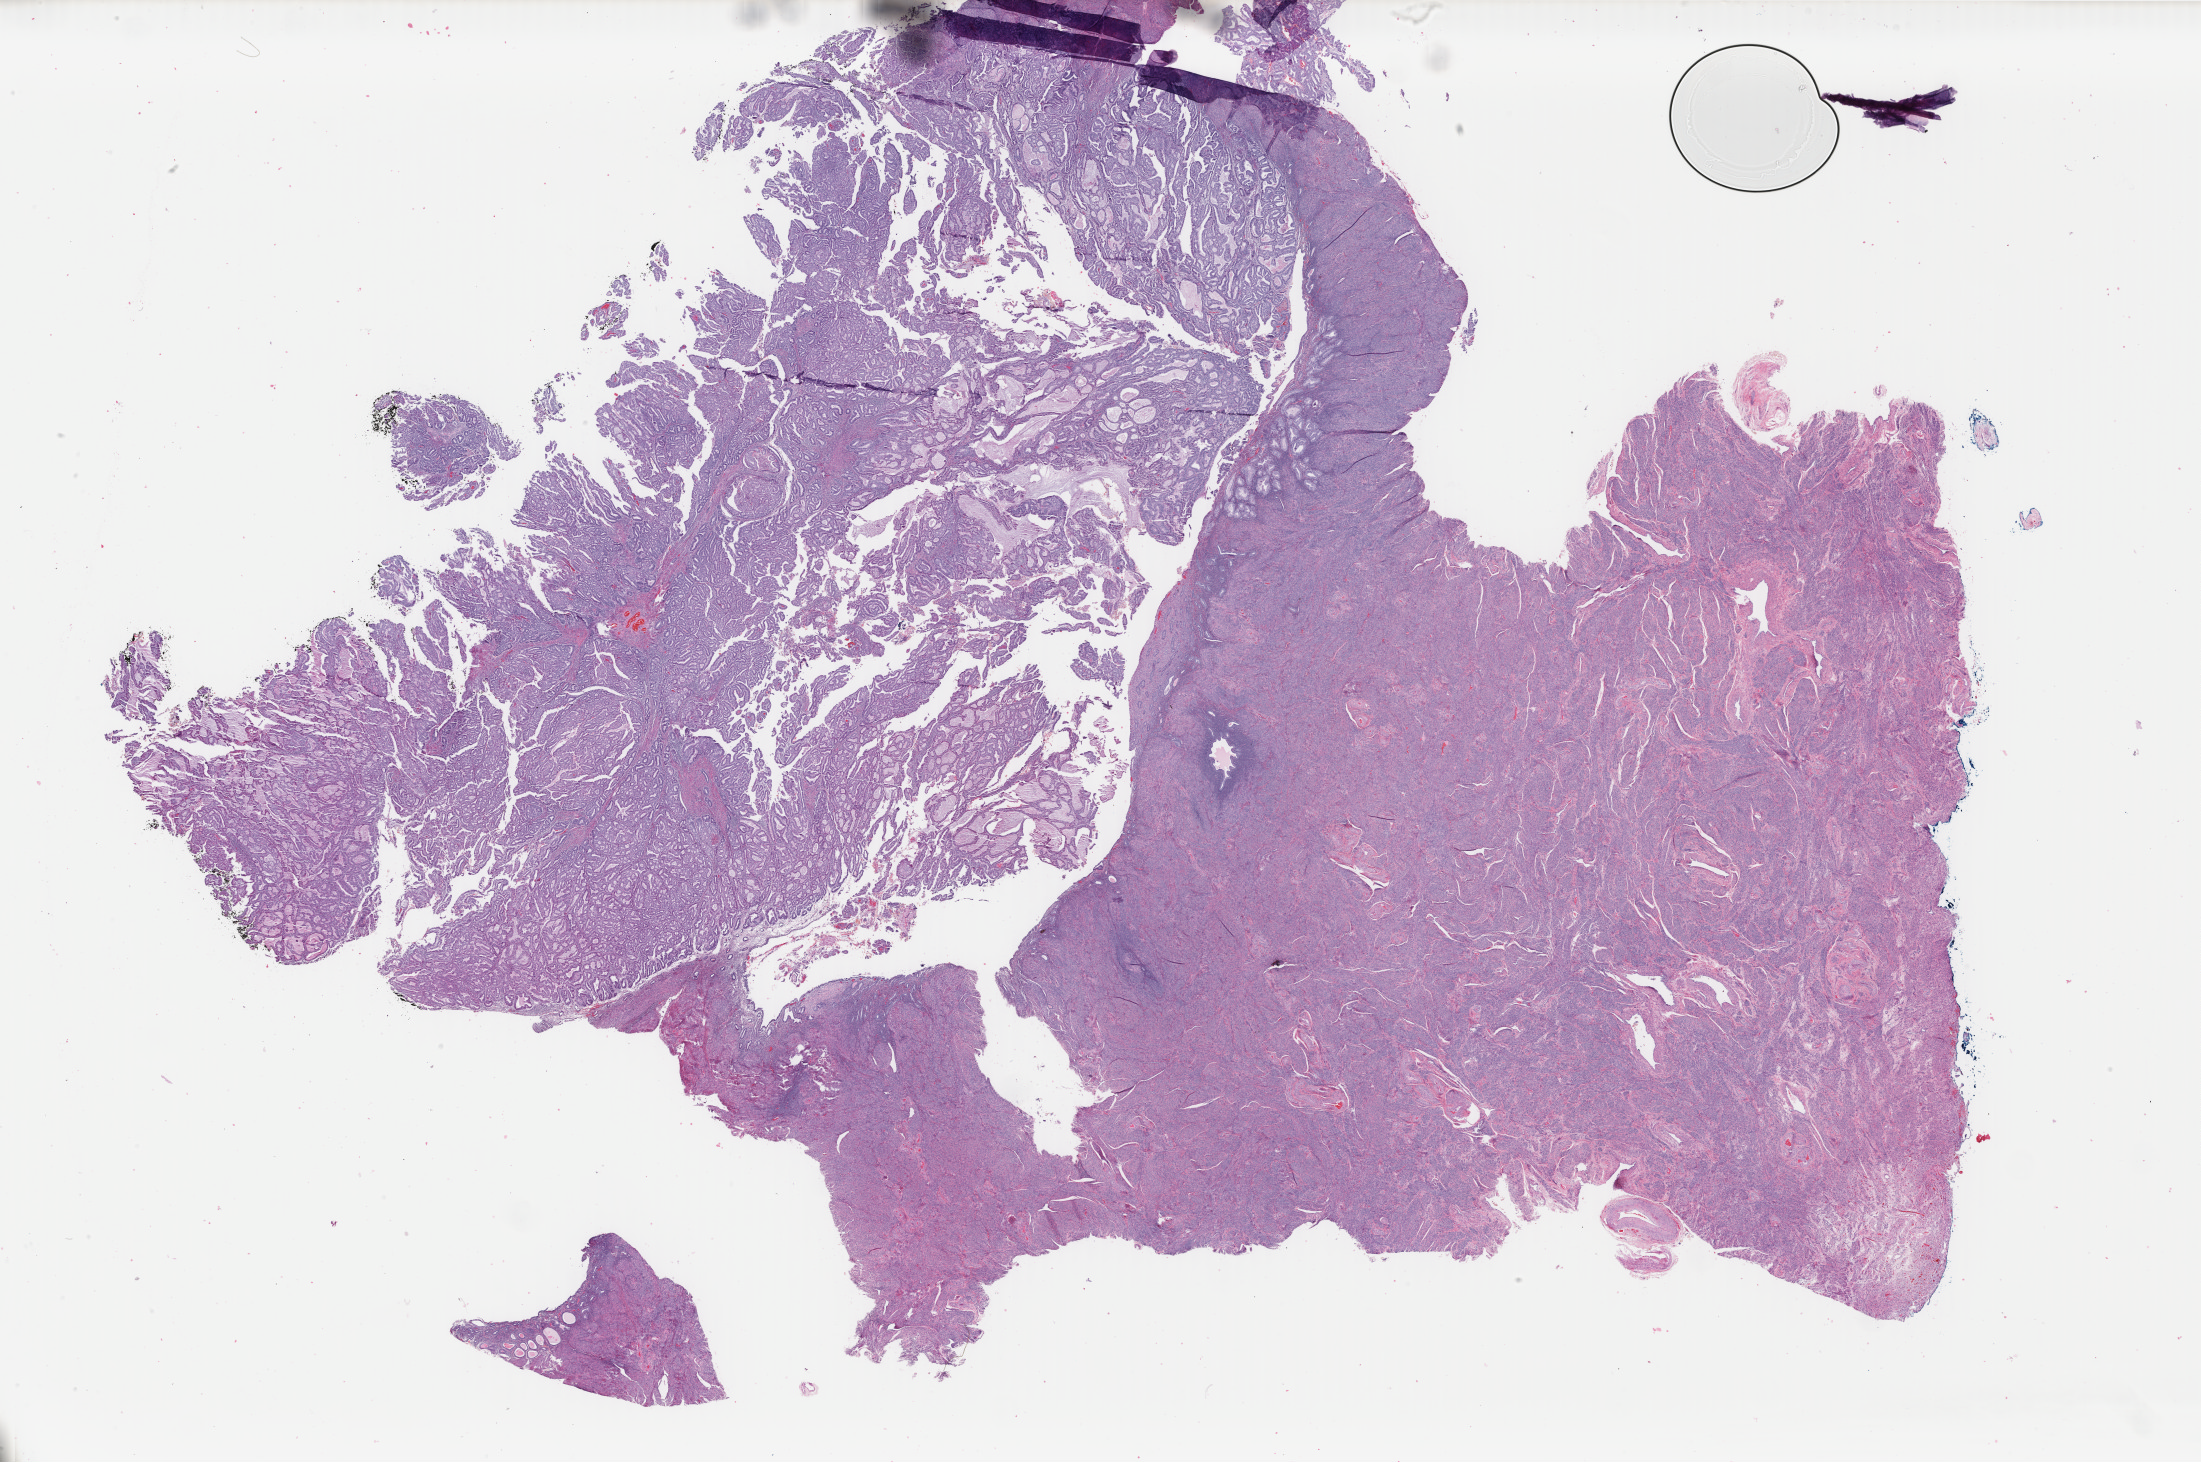
Digitized Hematoxylin and eosin (H&E) stained tissue section (whole slide), a low-resolution overview of the entire scanned area, about 34.9 x 23.2 mm. FFPE section. Sample: primary tumour, uterus. Female, age 54 years at initial diagnosis. Histologic grade: G1 (well differentiated).
- pathologic diagnosis: Endometrioid adenocarcinoma, NOS (endometrium)
- FIGO stage: IIIA